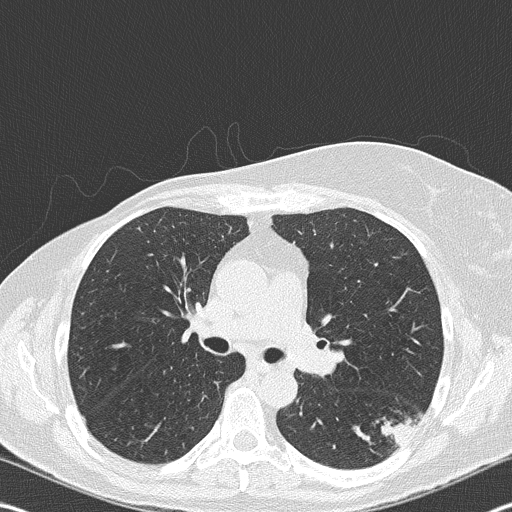
Low-dose screening chest CT, one axial slice; slice 111 of 177 in the series (ordered by position); reconstruction kernel B50f; 120 kVp; lung window (W 1500 / L -600 HU); 2 mm slice thickness; 512 × 512 image matrix.
Structures marked on this image (expert manual segmentation):
- lesion 1 (tumor): bounding box (x1, y1, x2, y2) in pixels: (381, 415, 420, 446)
- lesion 2 (nodule, hilum of left lung): (304, 350, 339, 374)